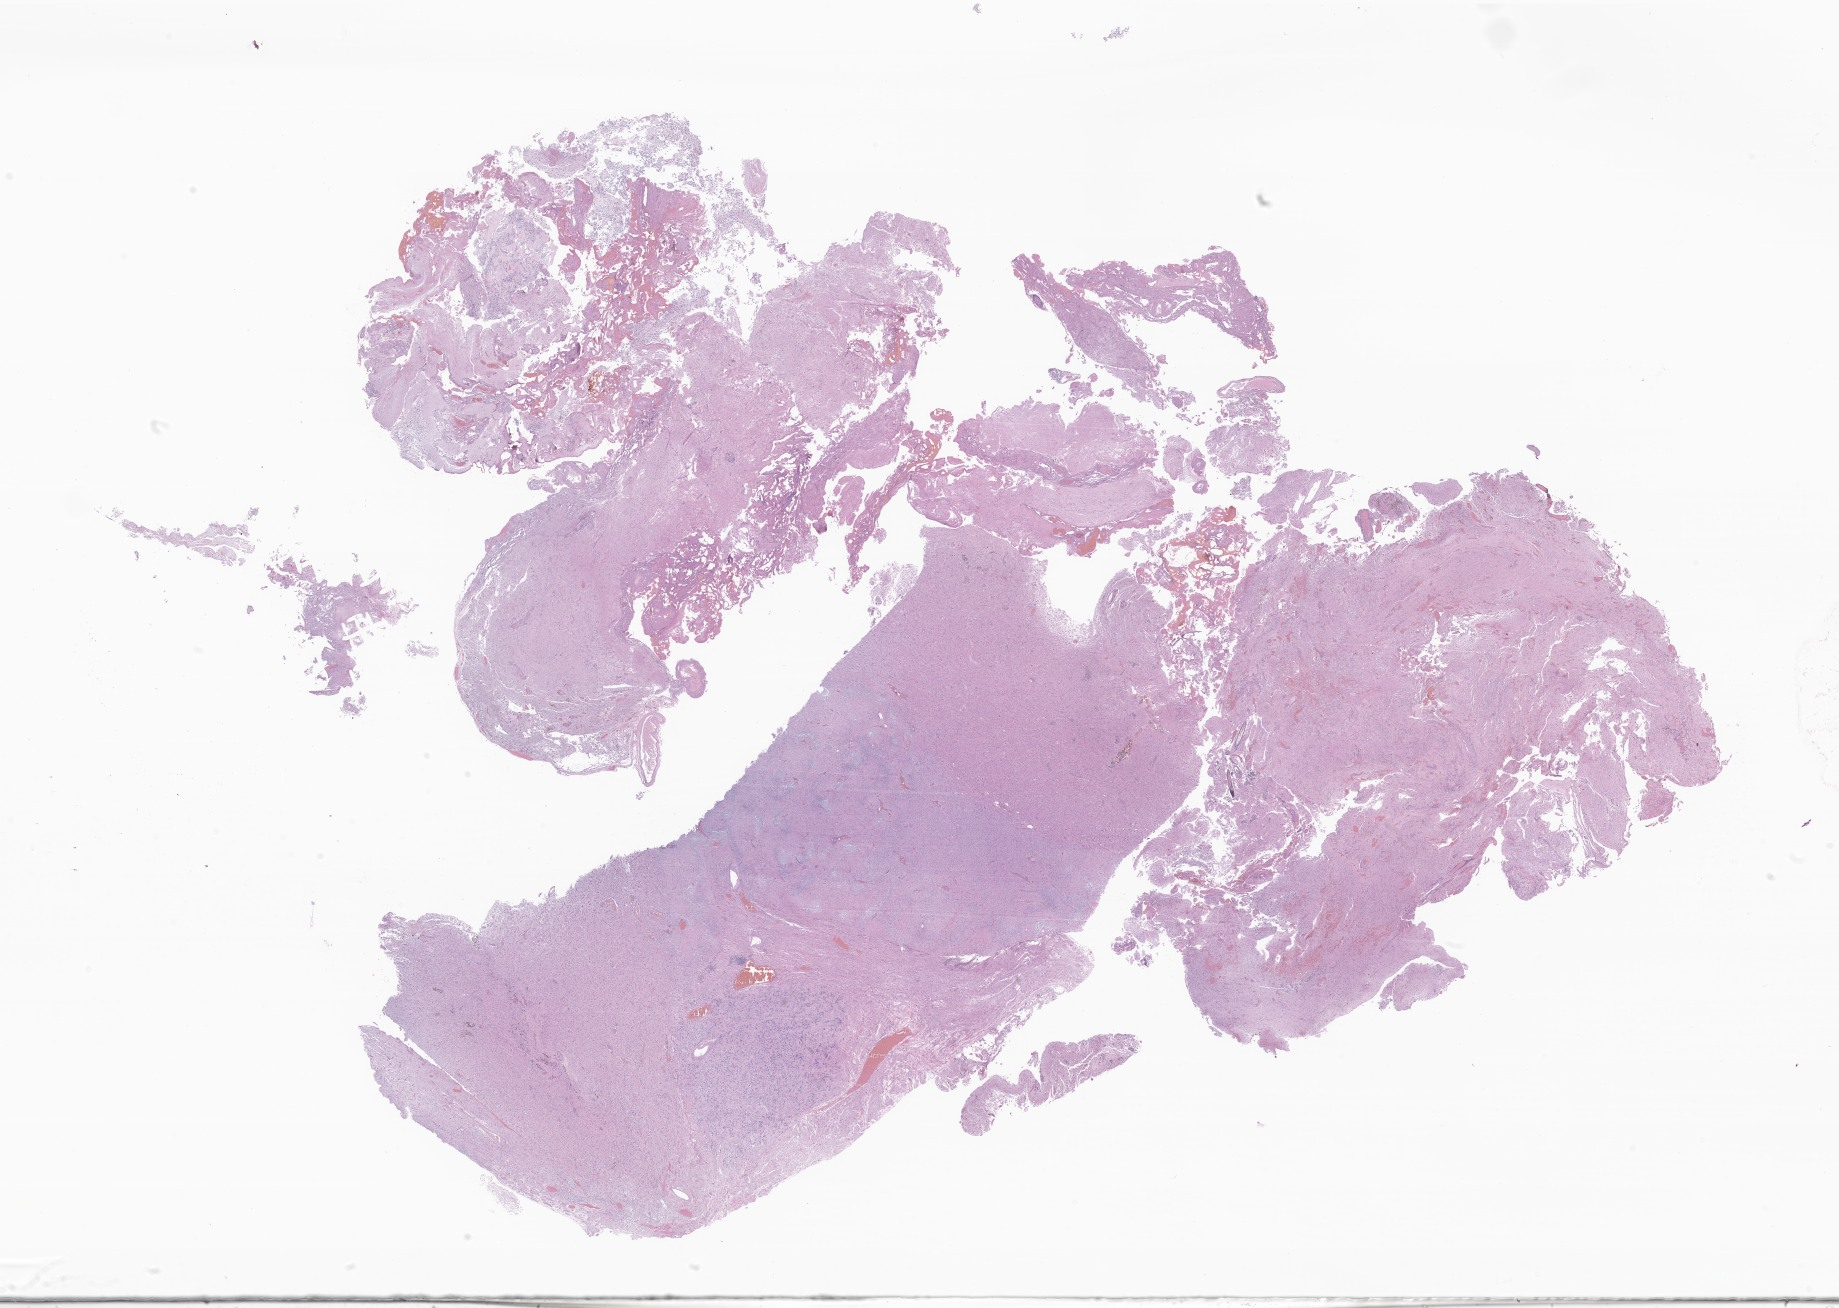
Whole-slide image, haematoxylin and eosin stain of tumor tissue from the brain, a low-resolution overview of the entire scanned area, about 31.0 x 22.1 mm; formalin-fixed, paraffin-embedded (FFPE) tissue. Patient male; age 159 months (13 years 3 months).
* diagnosis: Neoplasm, uncertain whether benign or malignant